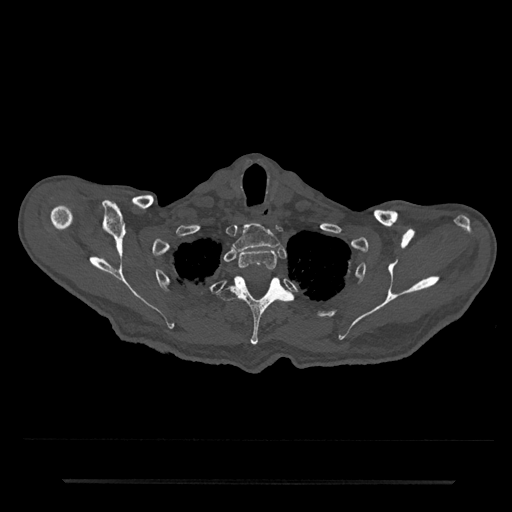
CT including the spine, one axial slice. Slice 679 of 797 in the series (ordered by position). Reconstruction kernel Br40s/3. 120 kVp. Bone window (W 1800 / L 400 HU). 0.5 mm slice thickness. 512 × 512 image matrix. Patient: male, 74 years. From the clinical record (not read from this slice): primary cancer: prostate.
Structures marked on this image (semi-automatic segmentation, software-assisted and operator-edited):
- T1 vertebra: bounding box [x1, y1, x2, y2] px = [232, 223, 280, 251]
- T2 vertebra: [238, 249, 277, 271]
- T3 vertebra: [218, 276, 293, 345]